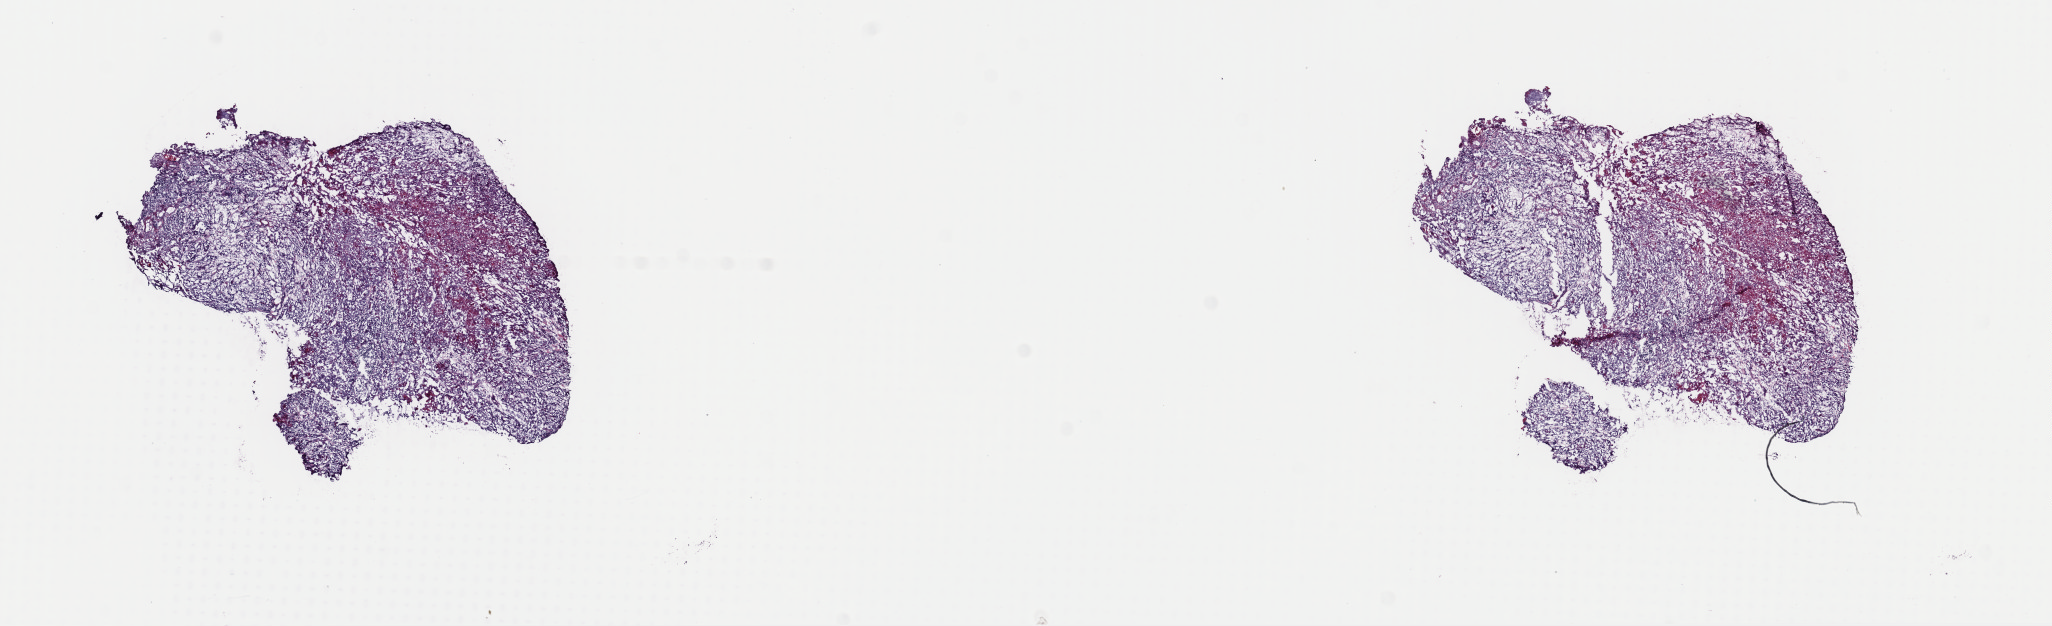
Digitized H&E-stained tissue section (whole slide), shown as a low-resolution overview of the whole scanned area (about 16.2 x 4.9 mm, from a 40x scan); frozen section from the top of the tissue portion; sample: primary tumour, head and neck. Male, age 63 years at initial diagnosis. Histologic grade: G2 (moderately differentiated). Slide review estimates, as recorded: tumour cells 85%, tumour nuclei 99%, normal cells 0%, stromal cells 5%, necrosis 10%. Inflammatory infiltration, as recorded: lymphocyte infiltration 0%, monocyte infiltration 0%, neutrophil infiltration 0%.
Lymph nodes positive (case pathology): 0 of 23 examined. TNM: T2 N0 M0. Diagnosis: Squamous cell carcinoma, NOS (cheek mucosa). AJCC pathologic stage: II.